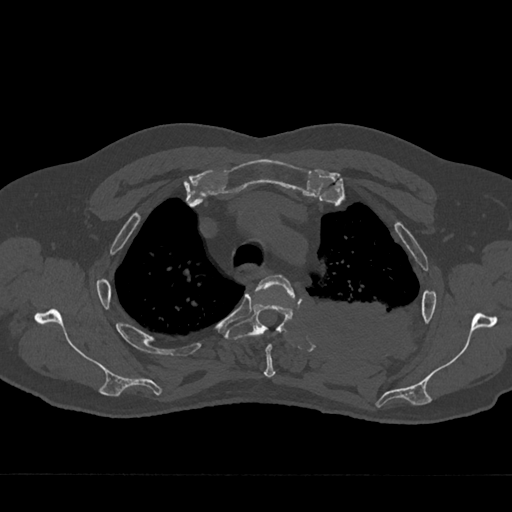
CT including the spine, one axial slice. Reconstruction kernel Br40s/3. 120 kVp. Bone window (W 1800 / L 400 HU). 0.5 mm slice thickness. 512 × 512 image matrix. Male patient, age 75 years. From the clinical record (not read from this slice): primary cancer: renal; vertebrae with lytic lesions (as recorded): T4.
Annotated regions visible in this slice (semi-automatic segmentation, software-assisted and operator-edited):
- T3 vertebra: box from (x=255, y=274) to (x=295, y=378) px
- T4 vertebra: (x=226, y=303)–(x=293, y=340)